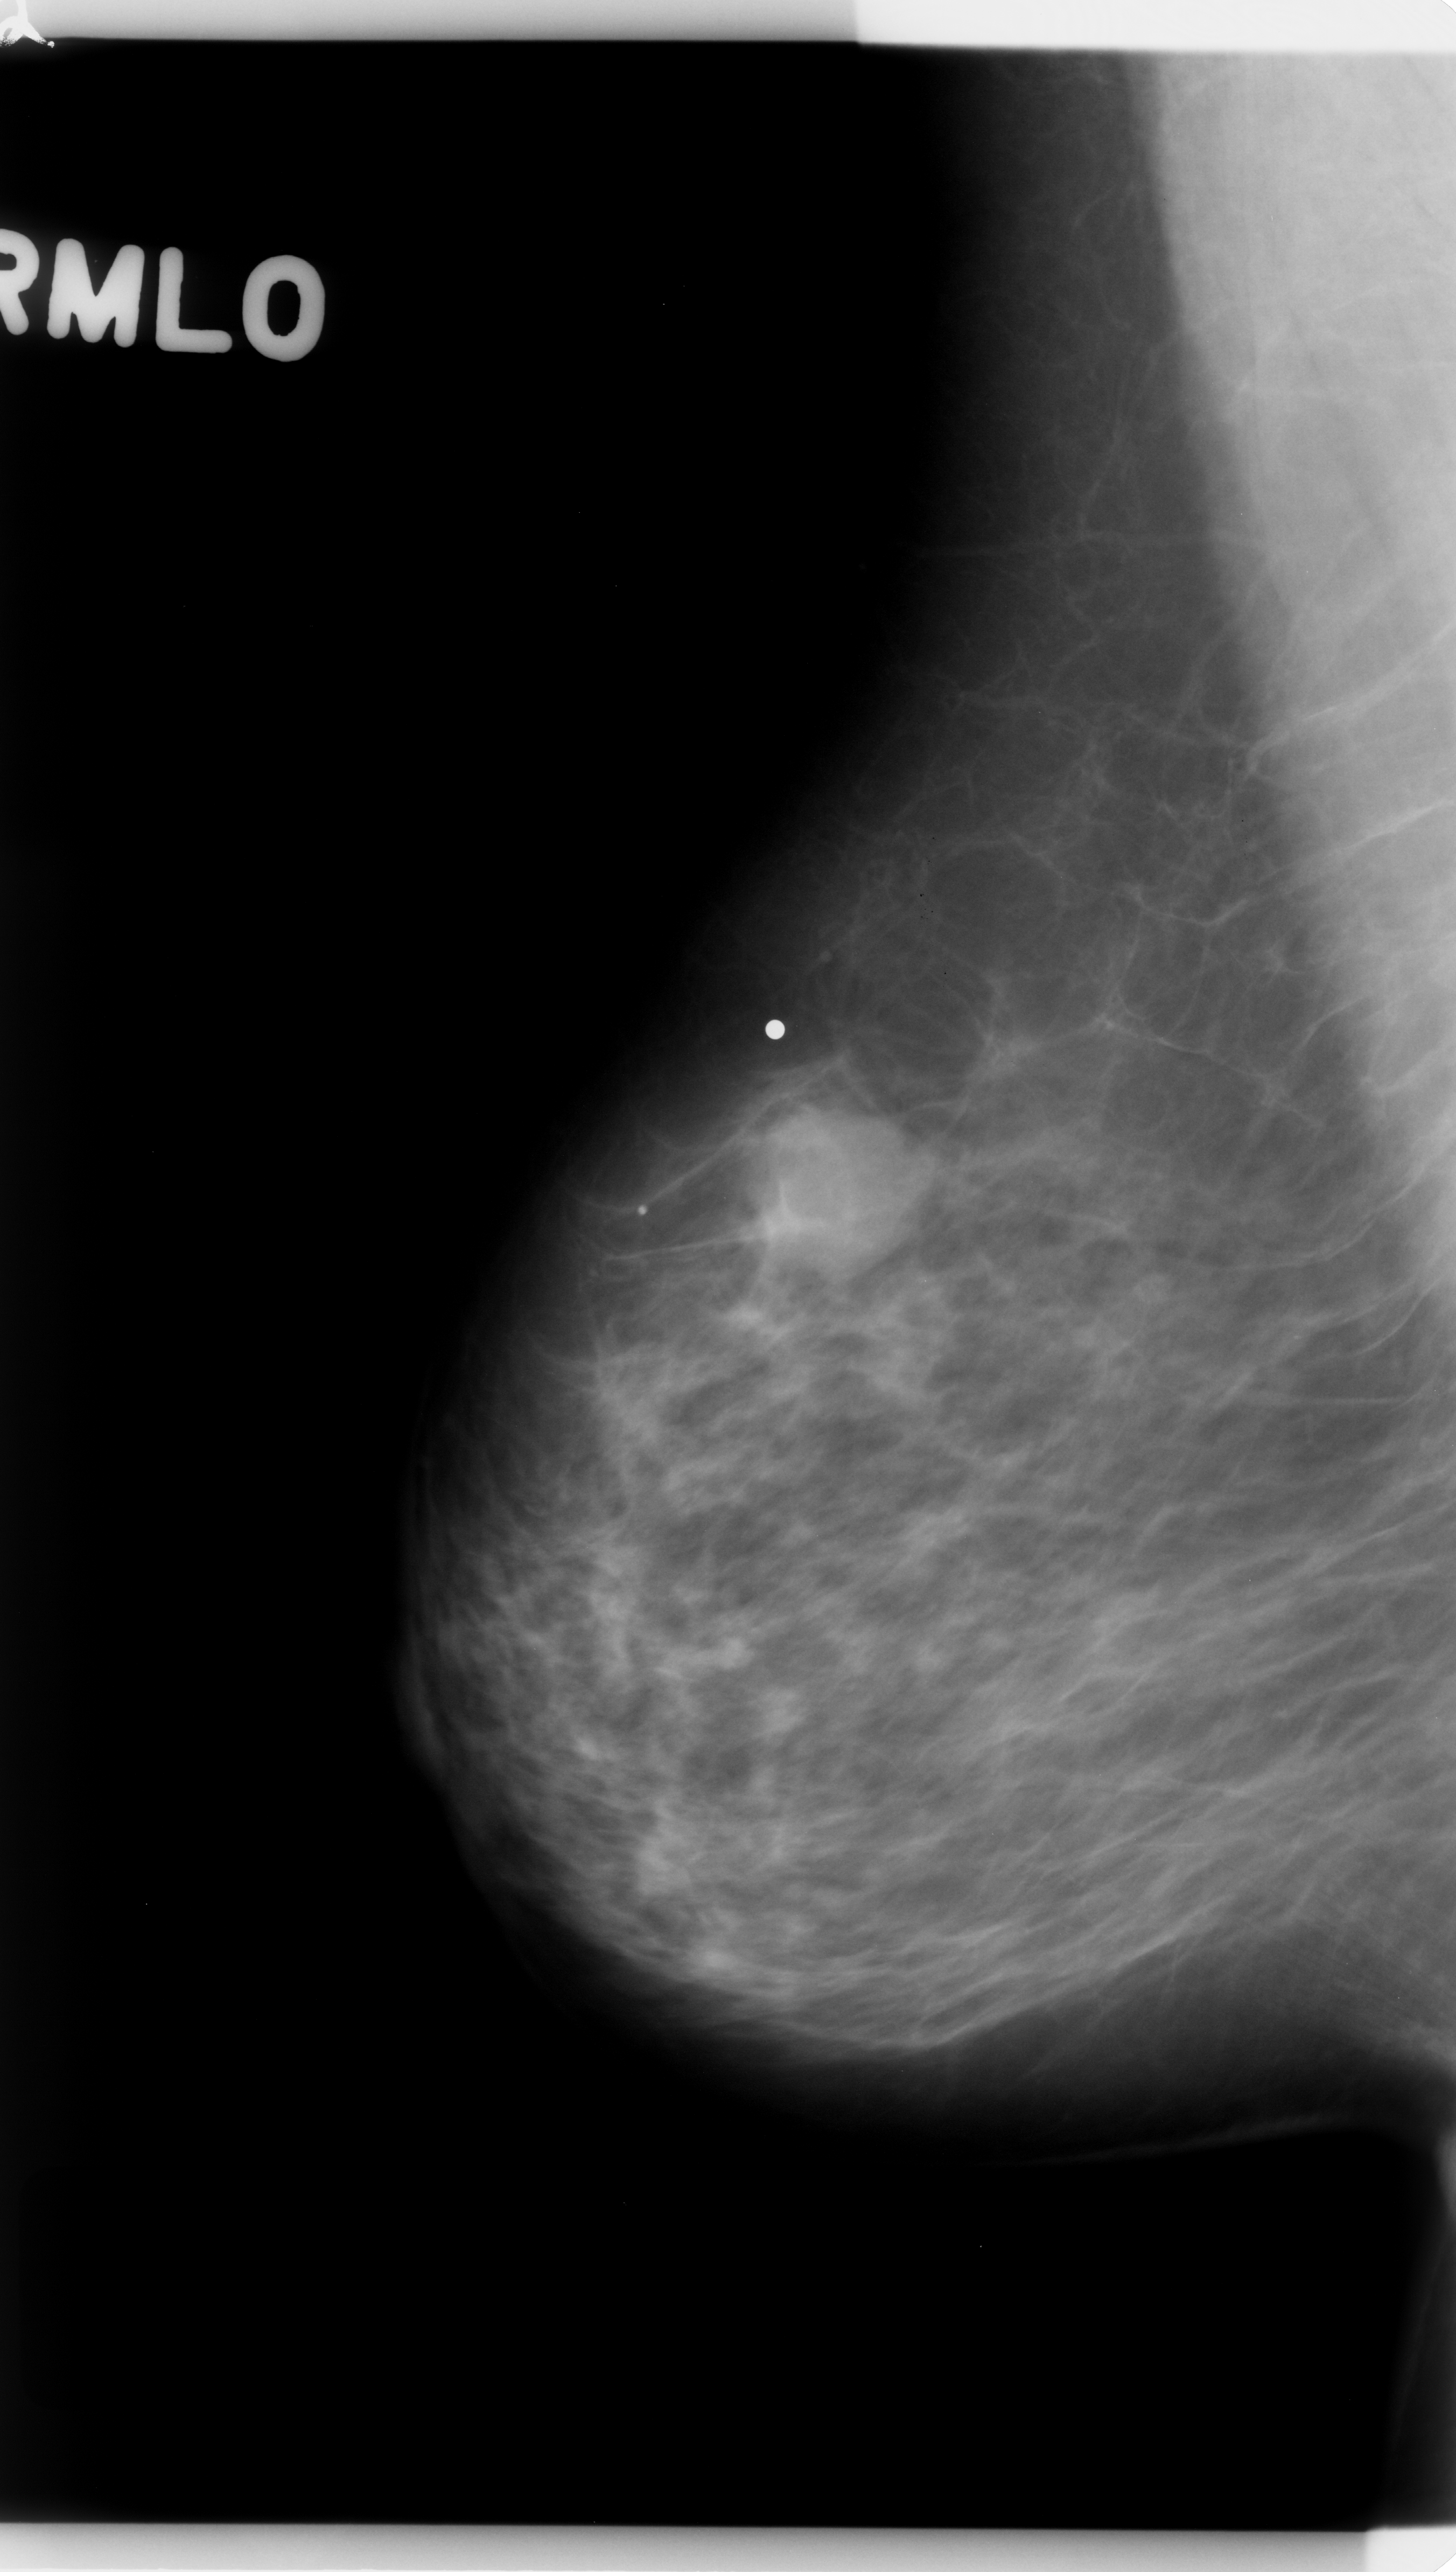
Mammogram (digitized film); right breast; mediolateral oblique (MLO) view; breast composition: scattered fibroglandular densities (BI-RADS density category 2 of 4).
- Finding: mass, shape round, margins microlobulated; BI-RADS assessment category 4; subtlety rating 5 on a 1 (subtle) to 5 (obvious) scale; pathology result (as recorded, not read from the image): benign.